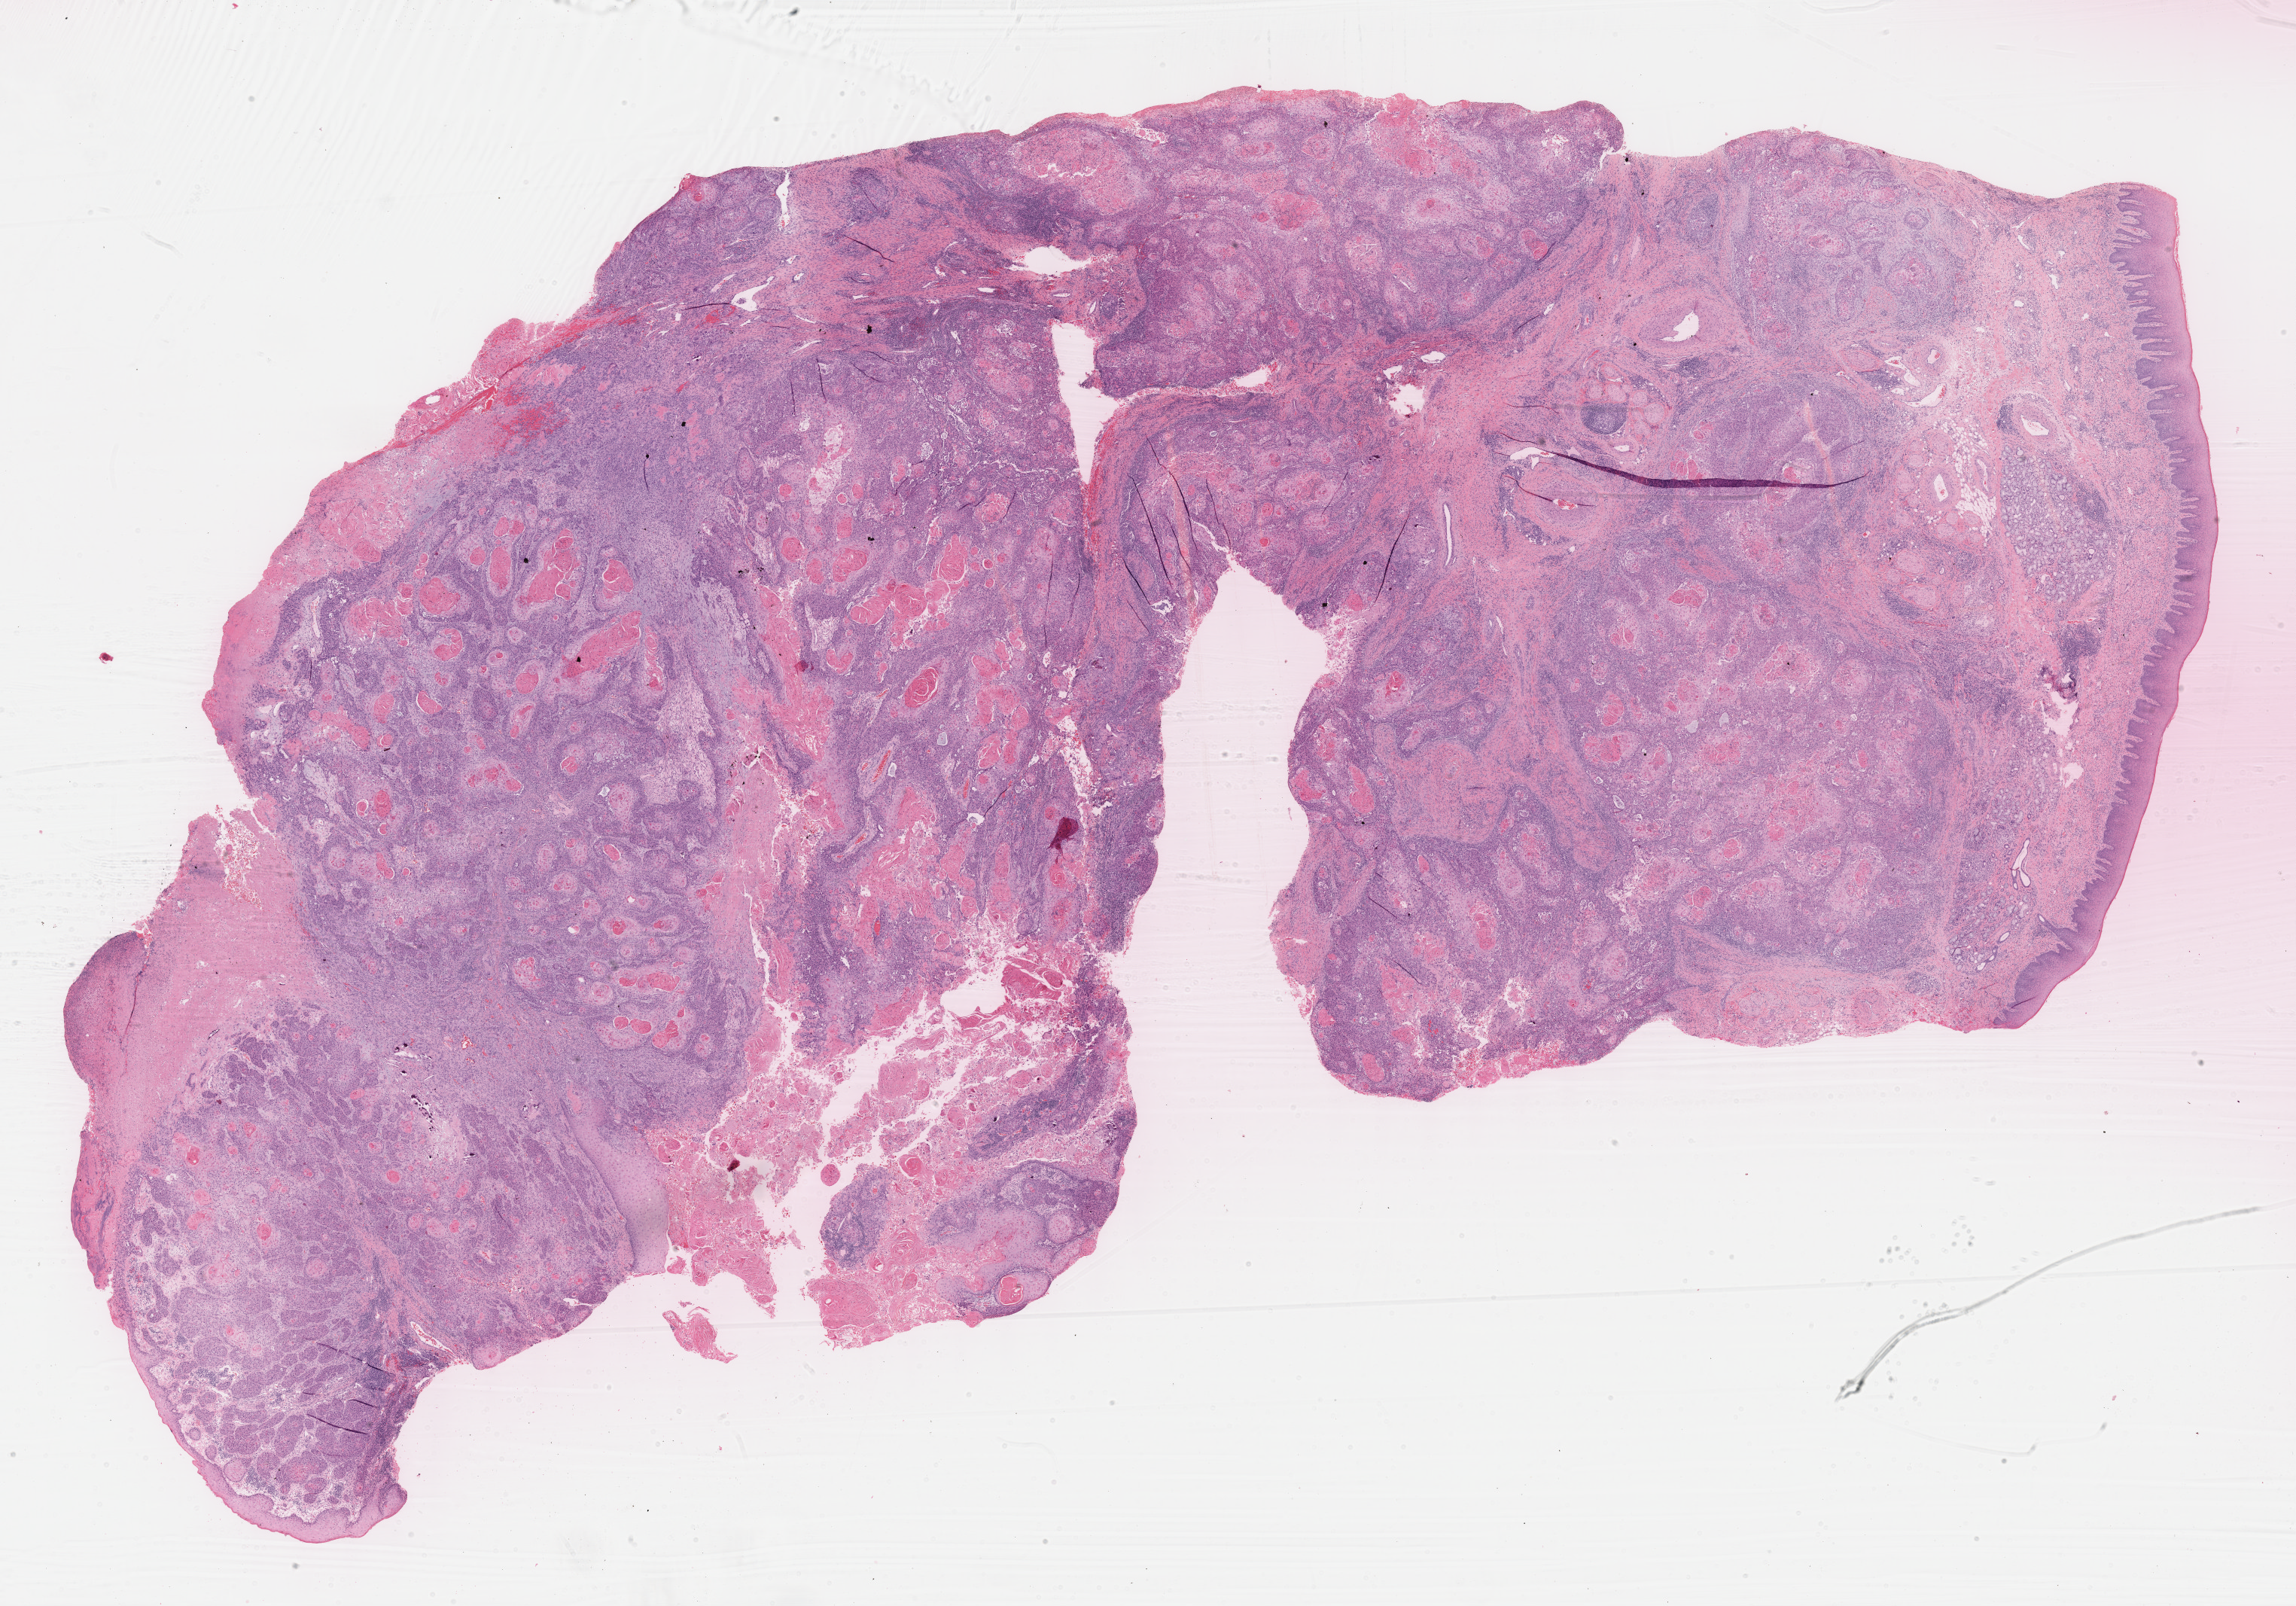
H&E whole-slide image — a low-resolution overview of the entire scanned area, about 24.6 x 17.2 mm (from a 40x scan), FFPE section, primary tumour sample from the head and neck. Male patient; age at initial diagnosis 39 years. Histologic grade: G2 (moderately differentiated).
AJCC pathologic stage: II (7th edition). Pathologic diagnosis: Squamous cell carcinoma, NOS (overlapping lesion of lip, oral cavity and pharynx).